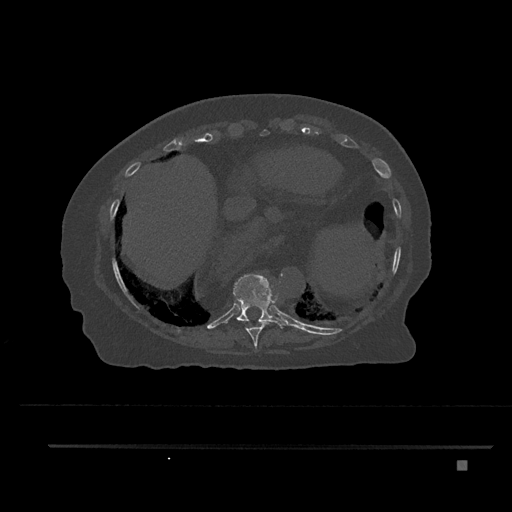
CT including the spine, one axial slice. Position 374 of 797 along the scan axis. Reconstruction kernel Br40s/3. Bone window (W 1800 / L 400 HU). 512 × 512 image matrix, field of view 437 × 437 mm. Female patient, age 76 years. Case-level facts recorded for this patient, not image findings: primary cancer: lung; vertebrae with lytic lesions (as recorded): T11, L3.
Annotated regions visible in this slice (semi-automatically segmented with operator editing):
- T10 vertebra: box from (x=229, y=273) to (x=290, y=328) px
- T9 vertebra: (x=238, y=320)–(x=268, y=347)